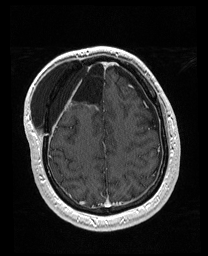
Brain MRI from a brain-tumour surgery series, one axial slice. Slice 54 of 176 in the series (ordered by position). T1-weighted post-contrast. 1 mm slice thickness. 208 × 256 image matrix. From the clinical record (not read from this slice): histopathology: Astrocytoma; WHO grade: 4.
Annotated regions visible in this slice (outlined manually by an expert reader):
- previous resection cavity: bounding box (x1, y1, x2, y2) in pixels: (69, 60, 101, 102)